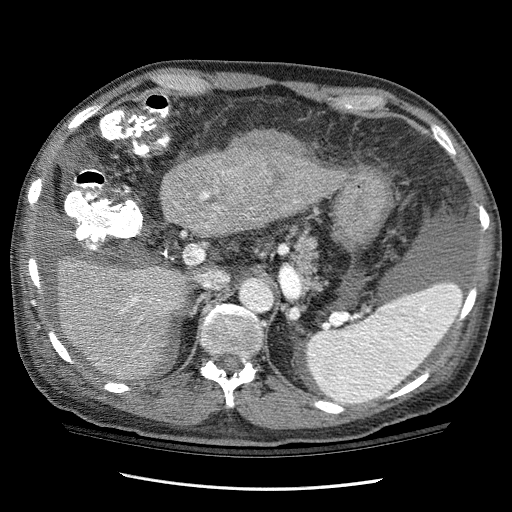
Contrast-enhanced abdominal CT (liver protocol), one axial slice. Slice 67 of 114 in the series (ordered by position). One of 3 acquisitions stored at this slice position. Soft-tissue window (W 400 / L 40 HU). 512 × 512 image matrix. From the clinical record (not read from this slice): diagnosis: hepatocellular carcinoma (patient treated with transarterial chemoembolisation; whether this scan precedes or follows treatment is not stated here); TNM stage (as recorded): Stage-I; Child-Pugh class: C; tumour nodularity: uninodular.
Annotated regions visible in this slice (semi-automatic segmentation, software-assisted and operator-edited):
- liver parenchyma outside the tumour (the mass and vessels are separate outlines, so this box may not span the whole liver): bounding box <38,141,348,380> (left, top, right, bottom; pixels)
- mass: <227,128,320,193>
- liver vessels: <122,193,209,351>